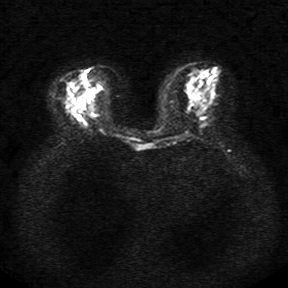
Breast MRI, one axial slice. Slice 11 of 34 in the series (ordered by position). Diffusion-weighted series; image 2 of 4 stored at this slice position (different b-values; order by instance number). 1.5 T. 5 mm slice thickness. 288 × 288 image matrix, field of view 340 × 340 mm. Female patient.
Outlined on this slice (manually delineated by an expert):
- tumour on diffusion-weighted imaging: bounding box <84,81,89,86> (left, top, right, bottom; pixels)